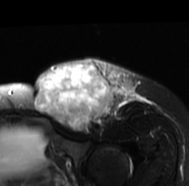
MRI of an extremity soft-tissue mass, one axial slice. Position 50 of 77 along the scan axis. T2-weighted fat-saturated. MR volume resampled by the dataset authors to the PET/CT grid (not the native acquisition matrix). 3.27 mm slice thickness. 189 × 186 image matrix, field of view 185 × 182 mm. Female patient. From the clinical record (not read from this slice): histological type: leiomyosarcoma; grade: high; site of the primary tumour: groin.
Structures marked on this image (expert contour drawn on MRI and transferred to this co-registered scan by the dataset authors):
- gross tumour volume including surrounding oedema: bounding box <33,57,148,133> (left, top, right, bottom; pixels)
- gross tumour volume (mass): <33,61,114,130>